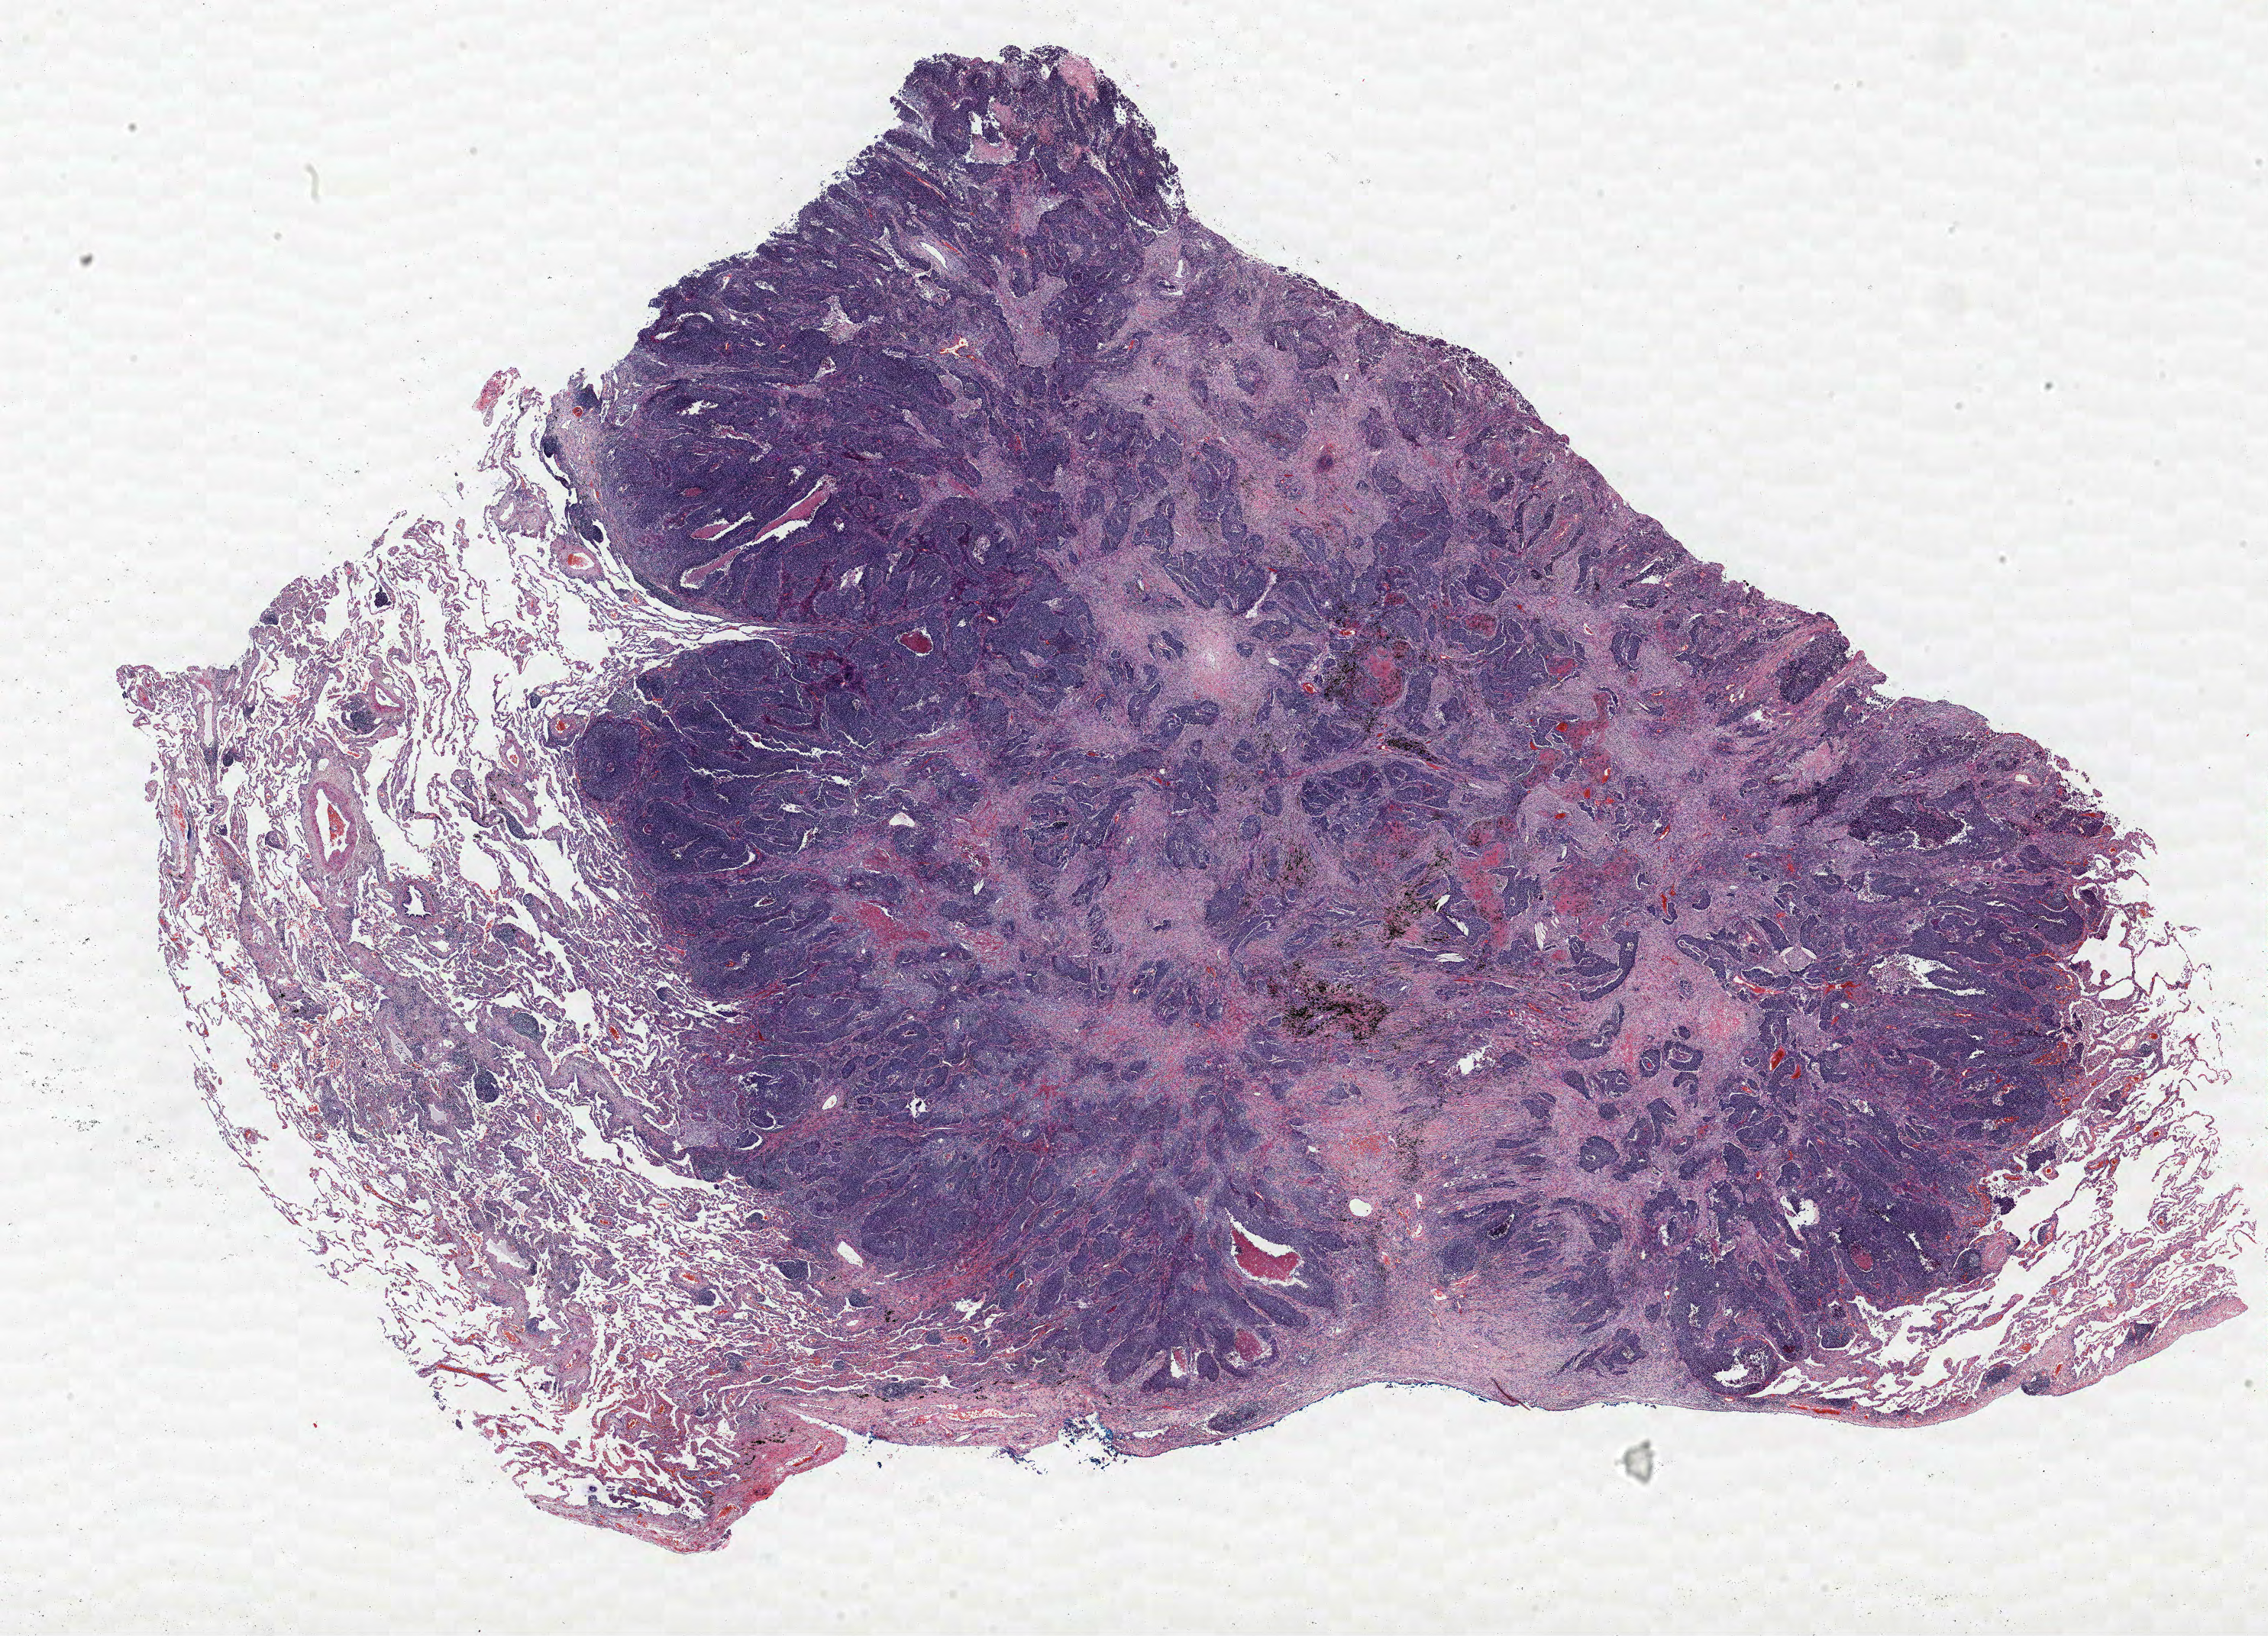
Whole-slide histology image, H&E-stained, whole scanned area (about 23.8 x 17.1 mm) shown as a low-resolution overview. Formalin-fixed paraffin-embedded (FFPE) section. Lung tissue. Male patient, aged 73 at enrolment. Former smoker at enrolment.
Participant's lung-cancer diagnosis: Adenocarcinoma, NOS (ICD-O-3 8140/3). Note: participant had 2 primary lung cancers recorded; fields above describe the first.